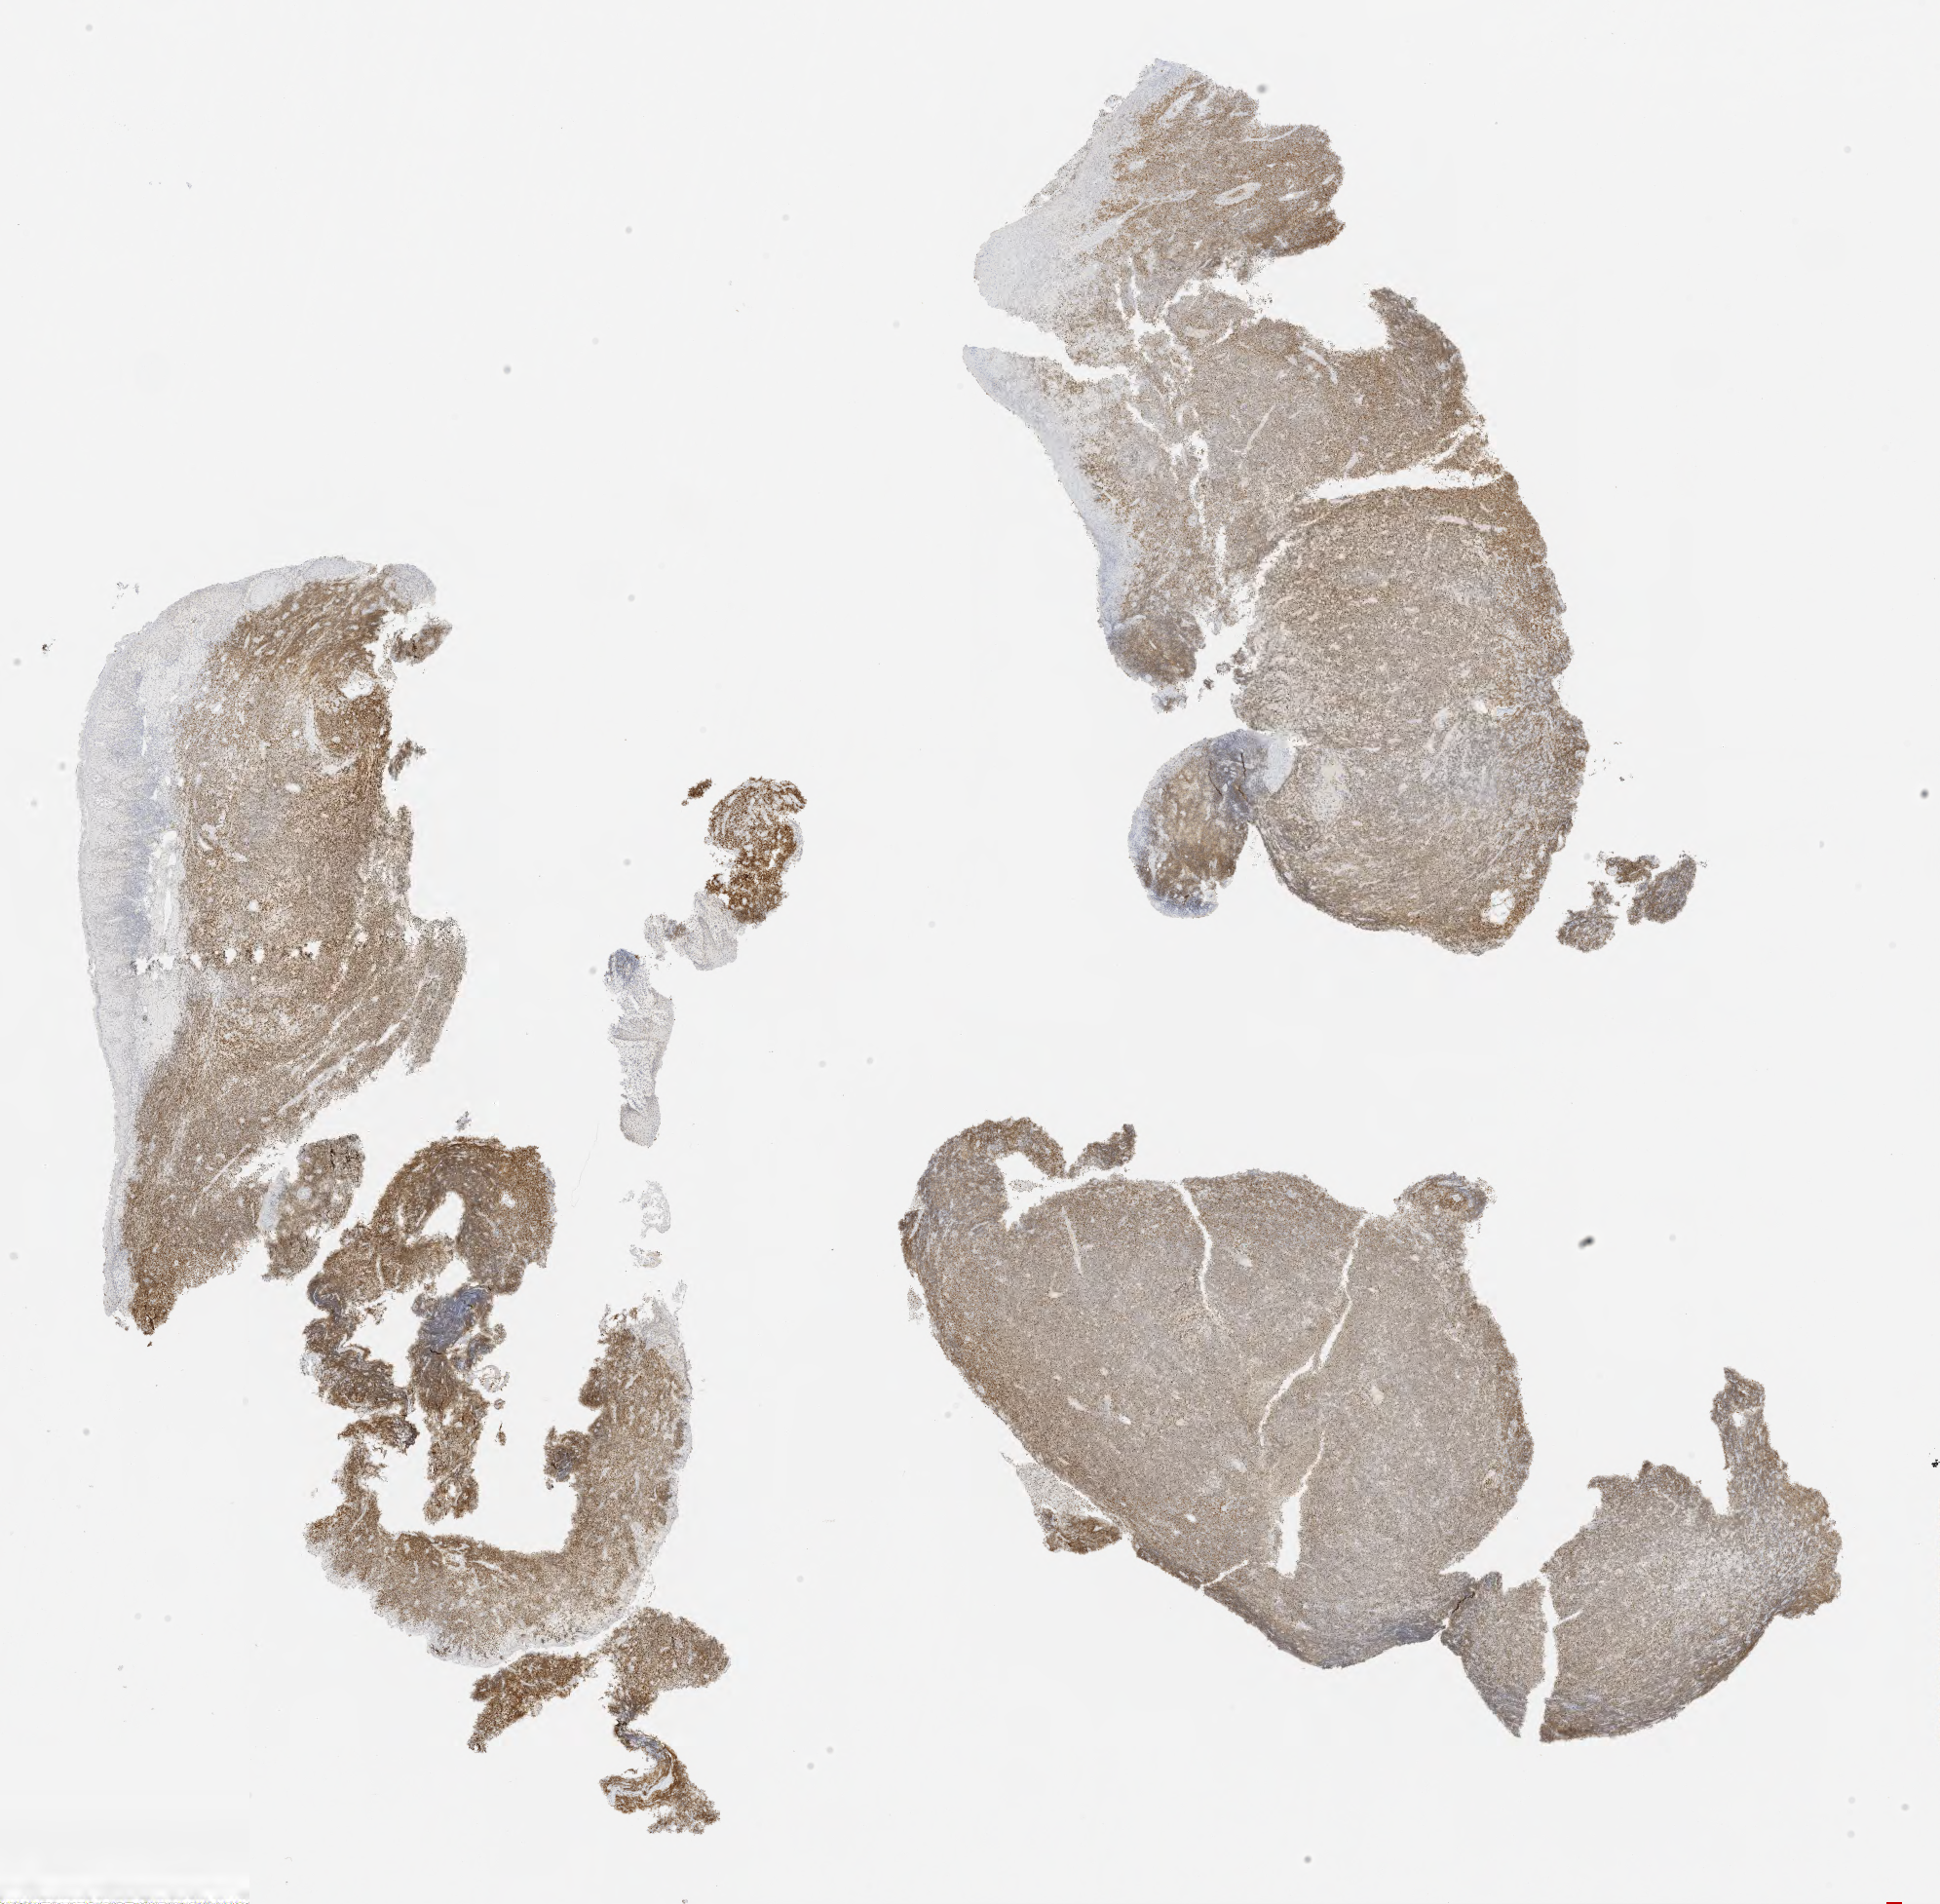
IHC for BCL6, whole-slide image, shown as a low-resolution overview of the whole scanned area (about 16.0 x 15.7 mm); specimen: tumor tissue. Patient male; age 22 years.
Diagnosis: Burkitt lymphoma, NOS.